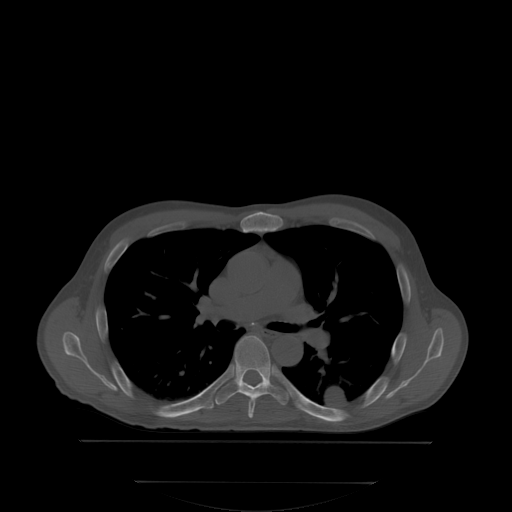
CT including the spine, one axial slice. Slice 239 of 350 in the series (ordered by position). Bone window (W 1800 / L 400 HU). 512 × 512 image matrix. Patient: male, 58 years. Case-level facts recorded for this patient, not image findings: primary cancer: prostate; vertebrae with lytic lesions (as recorded): L1.
Annotated regions visible in this slice (semi-automatic segmentation, software-assisted and operator-edited):
- T5 vertebra: bounding box [x1, y1, x2, y2] px = [250, 401, 255, 414]
- T6 vertebra: [216, 335, 289, 406]